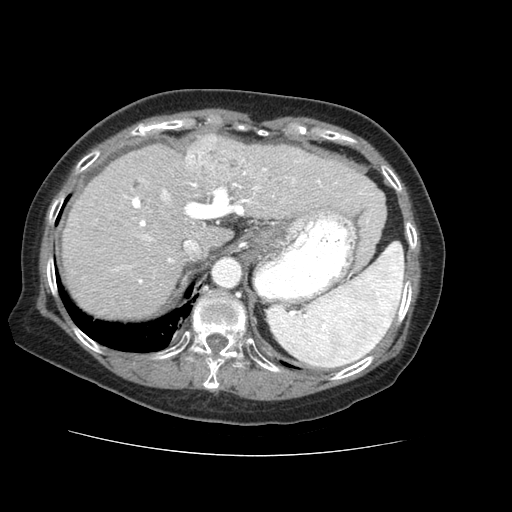
Contrast-enhanced abdominal CT (liver protocol), one axial slice; position 47 of 73 along the scan axis; soft-tissue window (W 400 / L 40 HU); 2.5 mm slice thickness; 512 × 512 image matrix, field of view 360 × 360 mm. Case-level facts recorded for this patient, not image findings: diagnosis: hepatocellular carcinoma (patient treated with transarterial chemoembolisation; whether this scan precedes or follows treatment is not stated here); TNM stage (as recorded): Stage-IVB; Child-Pugh class: A; tumour nodularity: uninodular.
Structures marked on this image (semi-automatically segmented with operator editing):
- liver parenchyma outside the tumour (the mass and vessels are separate outlines, so this box may not span the whole liver): bounding box [x1, y1, x2, y2] px = [62, 138, 384, 318]
- mass: [185, 134, 254, 182]
- liver vessels: [117, 161, 373, 284]